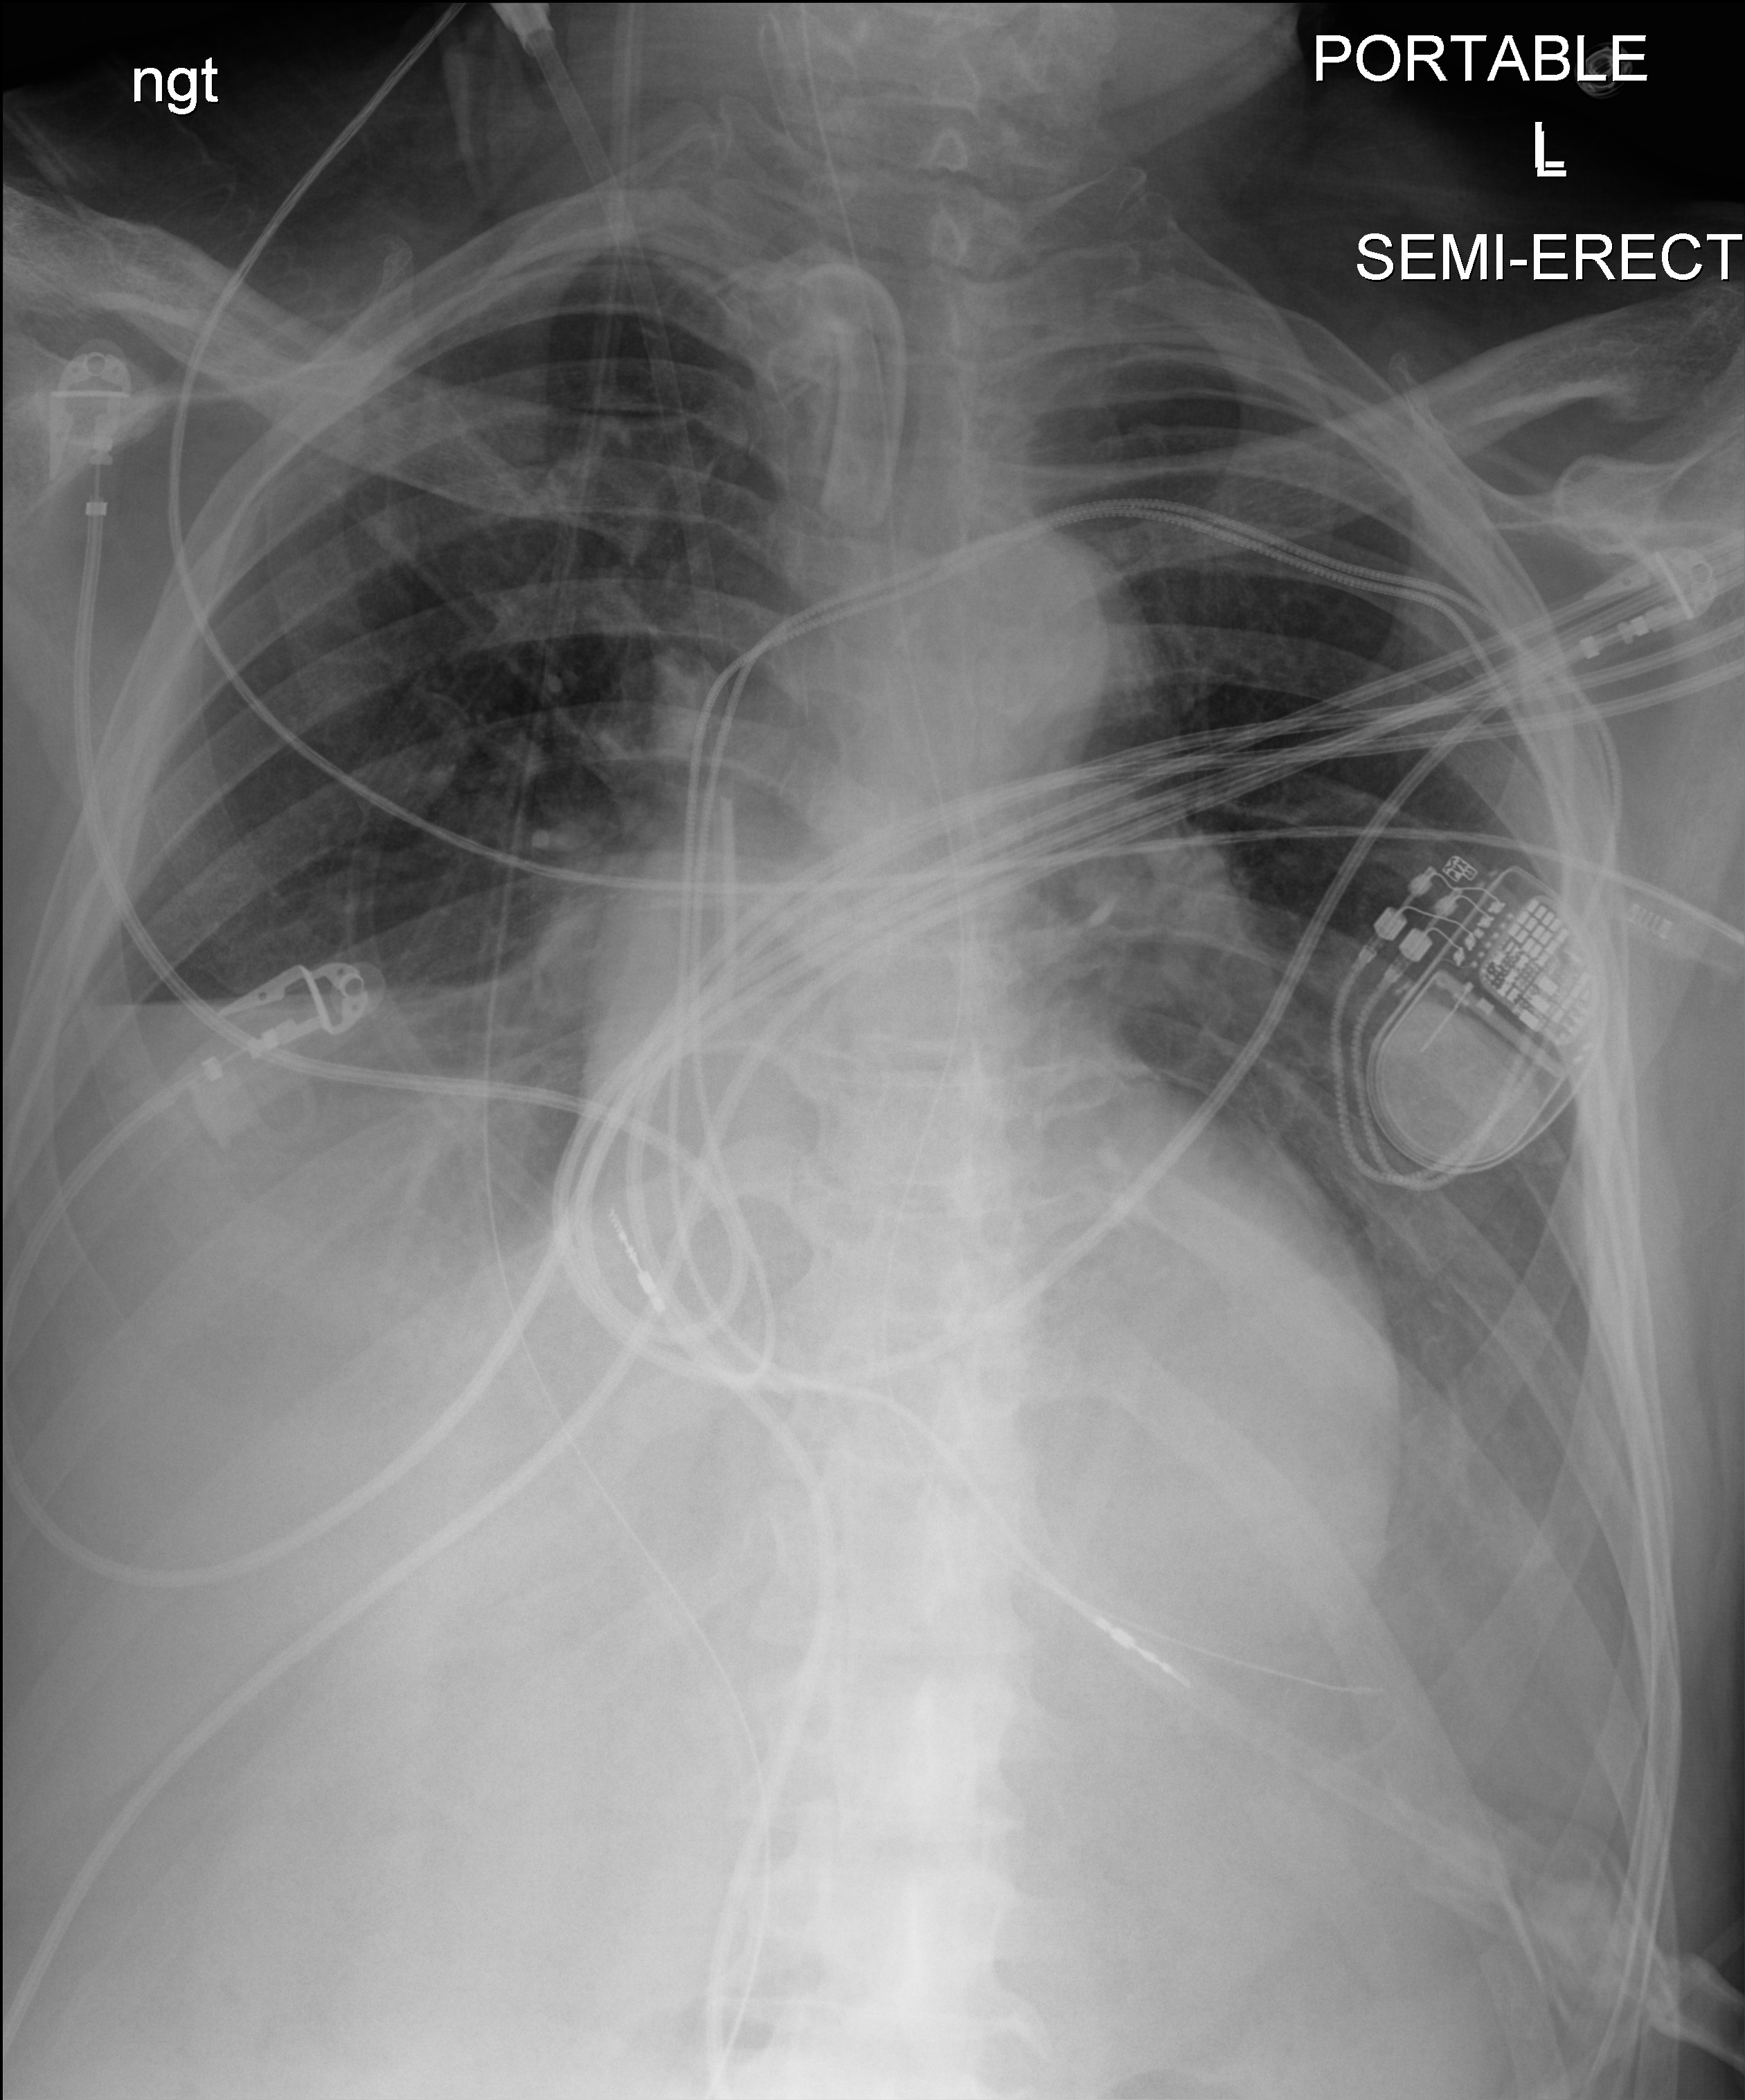
Chest X-ray (portable), anteroposterior (AP) projection. Male patient hospitalised with COVID-19, age 60–74 years.
From the hospital-stay record, not from the radiograph (when in the stay this image was taken is not recorded):
- mechanically ventilated during this hospital stay: yes